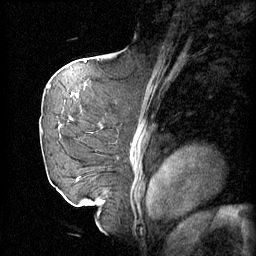
Breast MRI (dynamic contrast-enhanced), one sagittal slice; 4 images stored at this slice position (order not interpretable as contrast timing); 1.5 T; TE 4.2 ms, TR 11 ms; 256 × 256 image matrix. Female patient, age 72 years.
Structures marked on this image (semi-automatically segmented with operator editing):
- analysis volume of interest (the breast-tissue region the enhancement analysis was run in; not a lesion): bounding box <46,68,105,163> (left, top, right, bottom; pixels)
- tumour enhancement mask (voxels above the 70 % enhancement threshold inside the analysis volume of interest): <52,68,100,133>